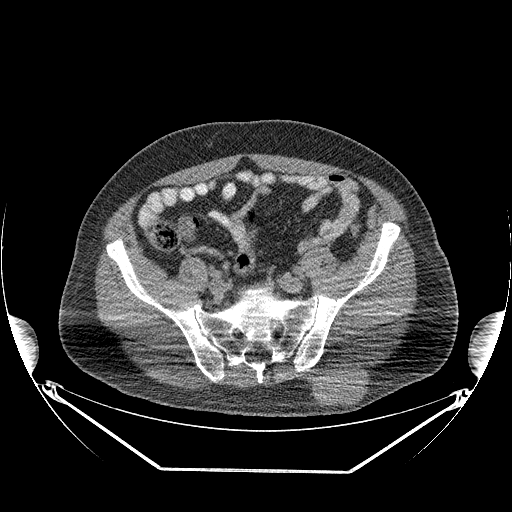
CT of an extremity soft-tissue mass (from a PET/CT study), one axial slice; slice 86 of 267 in the series (ordered by position); reconstruction kernel STANDARD; 140 kVp; soft-tissue window (W 400 / L 40 HU); 512 × 512 image matrix. Male patient. Case-level facts recorded for this patient, not image findings: histological type: pleiomorphic leiomyosarcoma; grade: high; site of the primary tumour: left buttock.
Structures marked on this image (expert contour drawn on MRI and transferred to this co-registered scan by the dataset authors):
- gross tumour volume including surrounding oedema: bounding box (x1, y1, x2, y2) in pixels: (310, 368, 368, 405)
- gross tumour volume (mass): (311, 370, 366, 405)